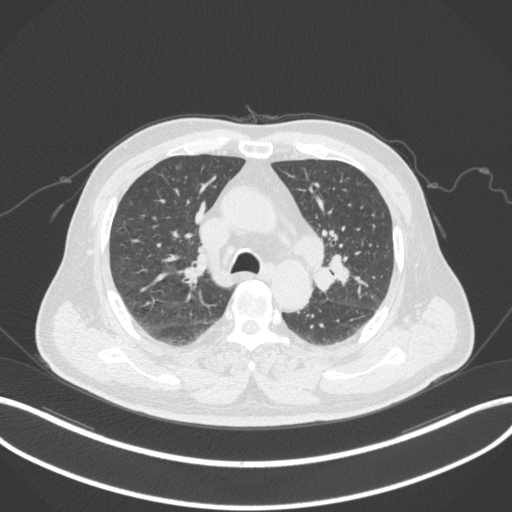
Chest CT, one axial slice; position 199 of 286 along the scan axis; reconstruction kernel B31f; 120 kVp; lung window (W 1500 / L -600 HU); 1 mm slice thickness; 512 × 512 image matrix. Patient: male, 67 years. Case-level facts recorded for this patient, not image findings: clinical TNM (as recorded): T2a N1 M0.
Annotated regions visible in this slice (bounding box drawn by a radiologist):
- lung tumour (recorded histology: adenocarcinoma): bounding box (x1, y1, x2, y2) in pixels: (311, 252, 351, 290)